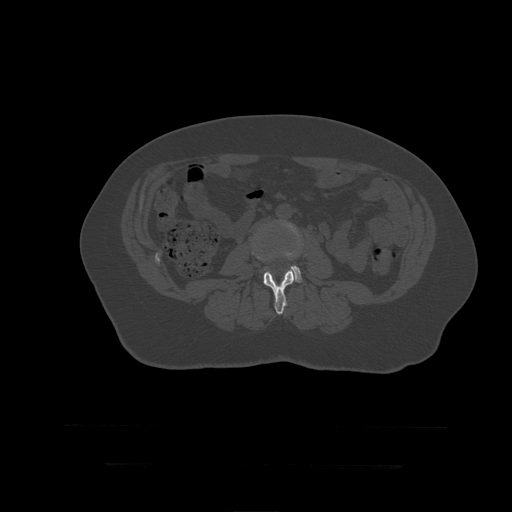
CT including the spine, one axial slice; slice 113 of 399 in the series (ordered by position); bone window (W 1800 / L 400 HU); 1.25 mm slice thickness; 512 × 512 image matrix. Patient age 41 years. Case-level facts recorded for this patient, not image findings: primary cancer: breast.
Annotated regions visible in this slice (semi-automatic segmentation, software-assisted and operator-edited):
- L3 vertebra: bounding box <252,252,297,315> (left, top, right, bottom; pixels)
- L4 vertebra: <266,222,302,283>